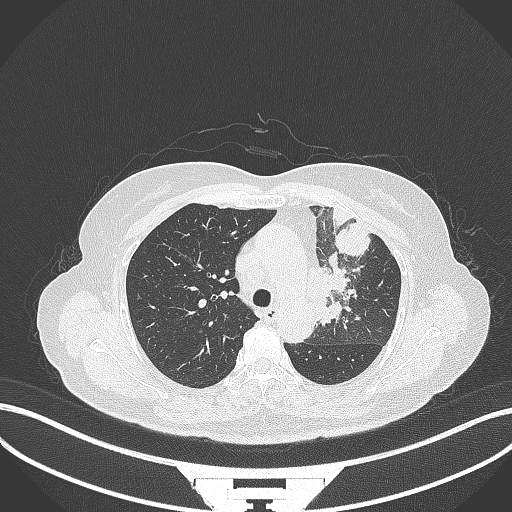
Chest CT, one axial slice. Position 236 of 382 along the scan axis. Reconstruction kernel B70f. 120 kVp. Lung window (W 1500 / L -600 HU). 512 × 512 image matrix, field of view 400 × 400 mm. Female patient, age 64 years. Case-level facts recorded for this patient, not image findings: clinical TNM (as recorded): T2a N2 M0.
Annotated regions visible in this slice (bounding box drawn by a radiologist):
- lung tumour (recorded histology: adenocarcinoma): bounding box (x1, y1, x2, y2) in pixels: (308, 257, 355, 327)
- lung tumour (recorded histology: adenocarcinoma): (334, 218, 374, 257)